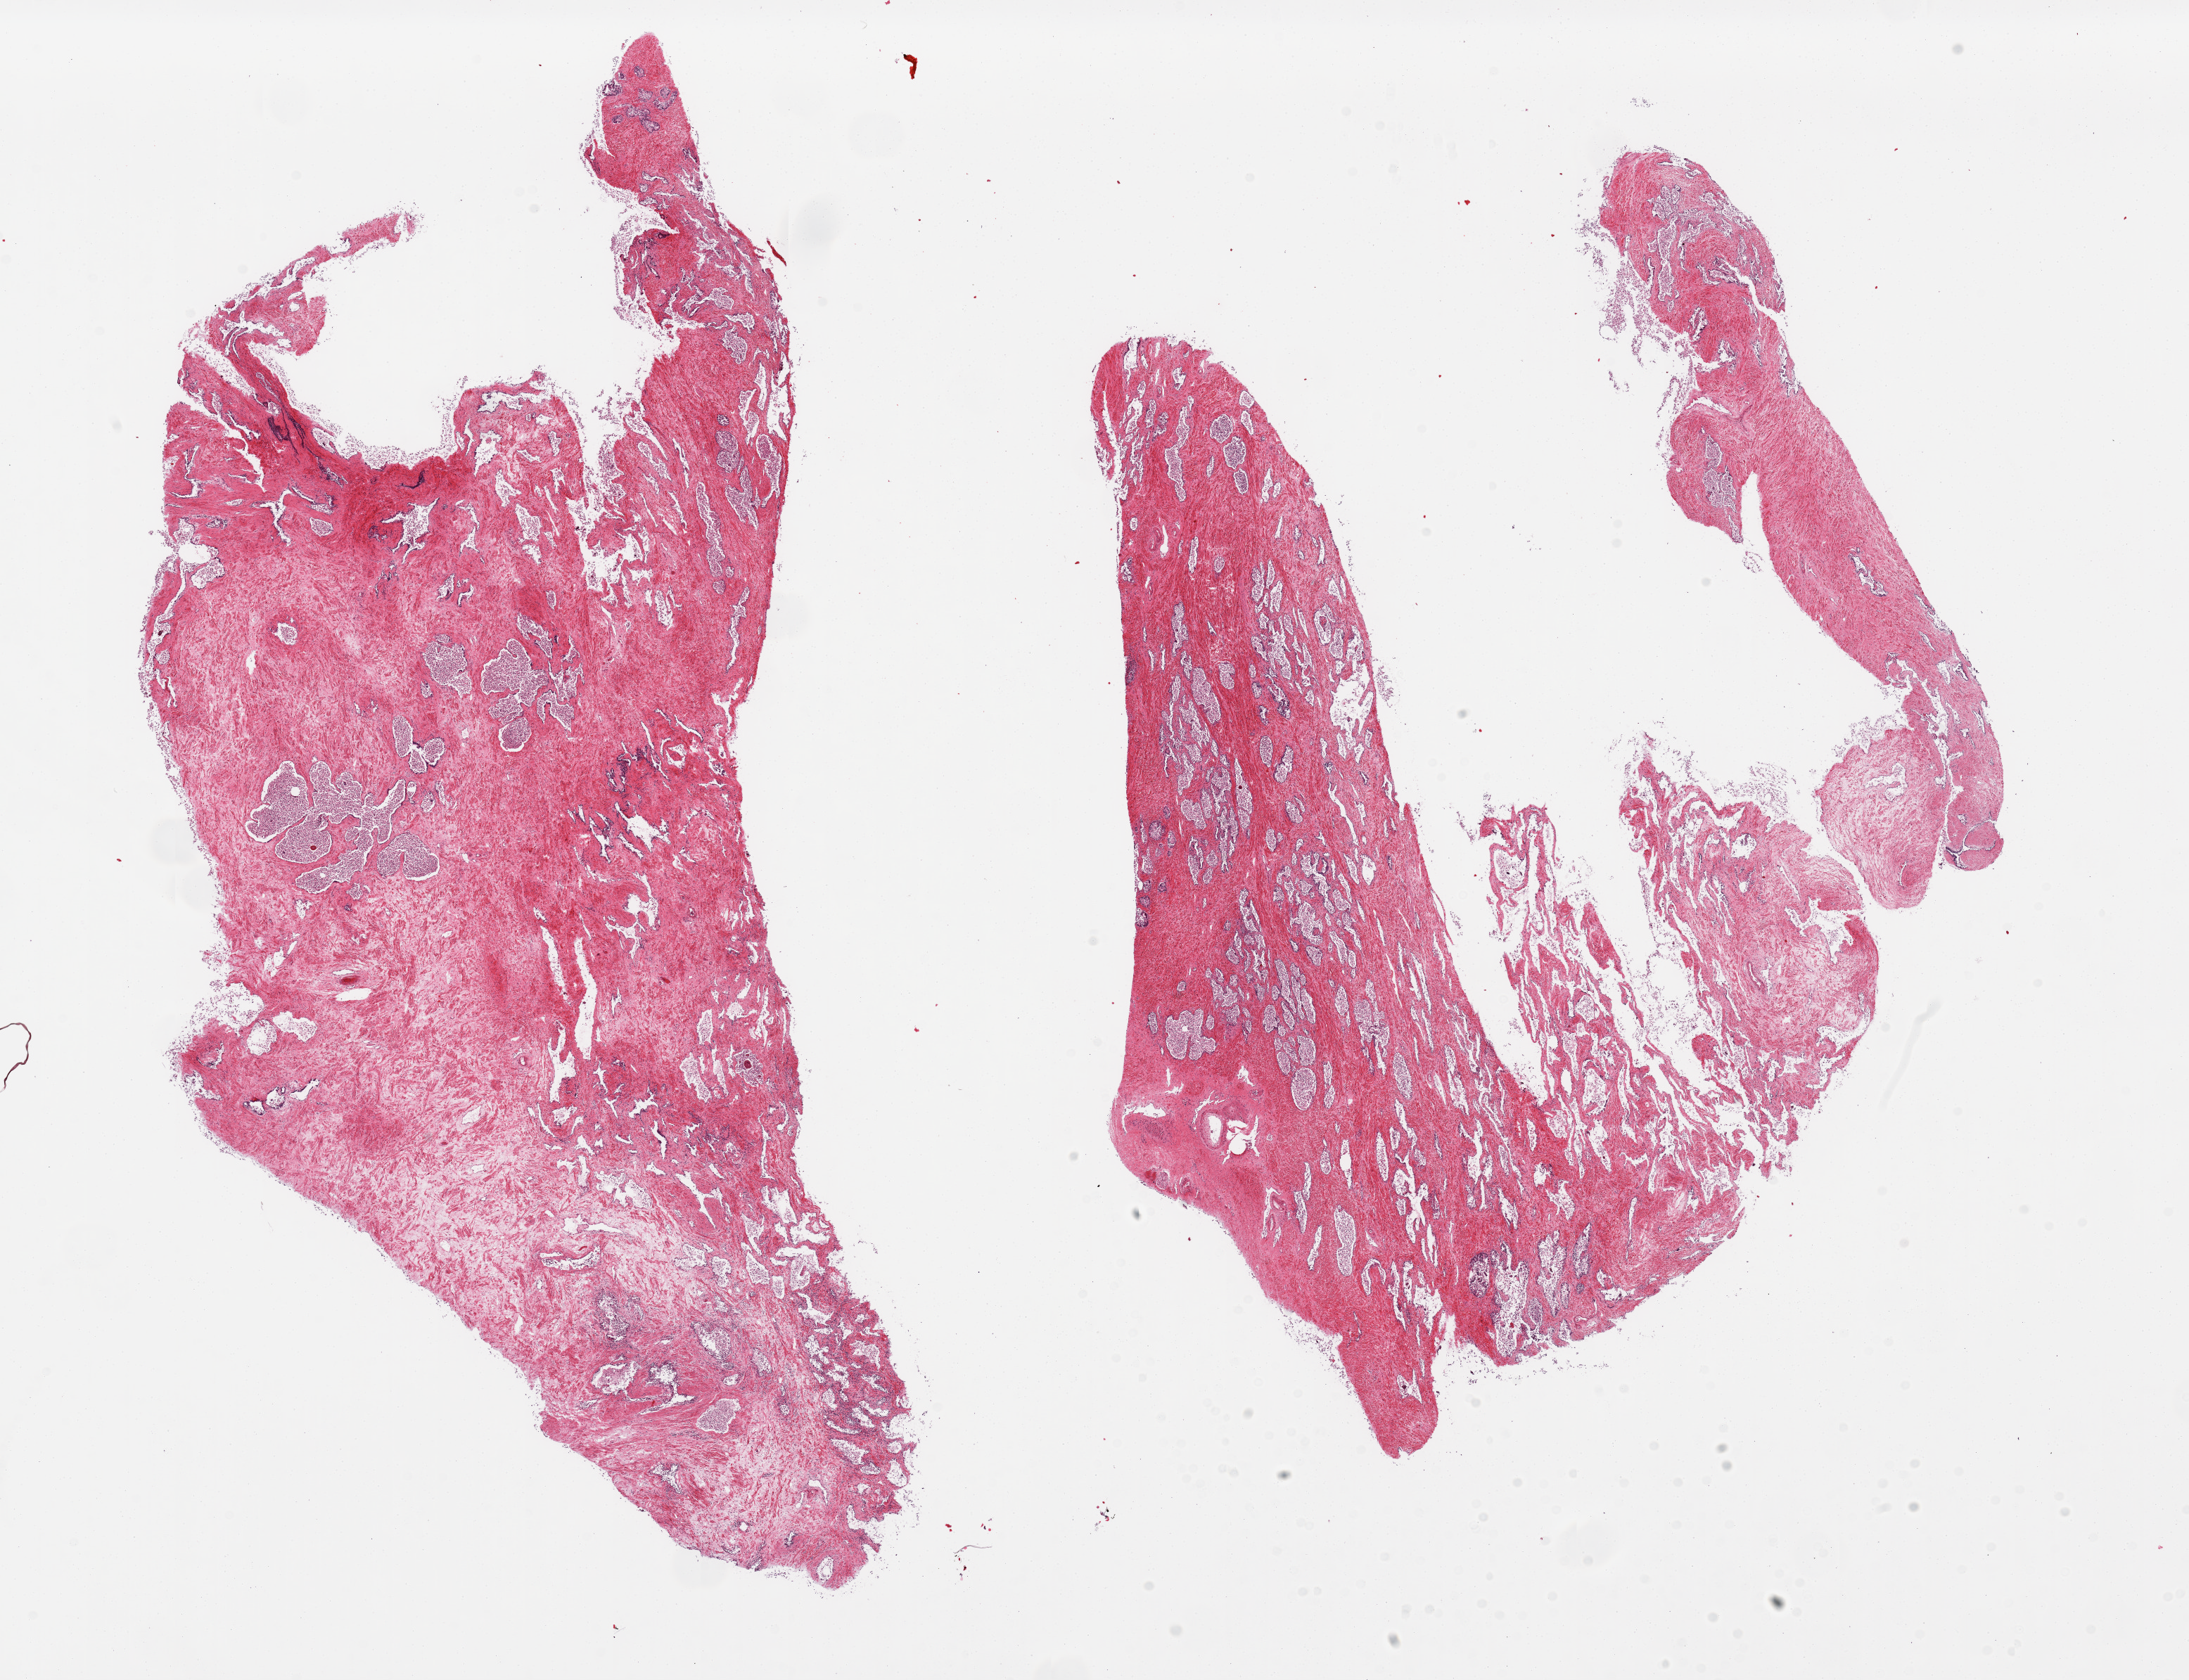
Haematoxylin and eosin whole-slide image, brightfield, a low-resolution overview of the entire scanned area, about 24.6 x 18.9 mm. PAXgene-fixed paraffin-embedded (PFPE) section. Sampled site (target tissue): prostate. Donor tissue sample. Male donor.
Review note (as recorded): 2 pieces, epithelium sloughed, glands represent ~25%.